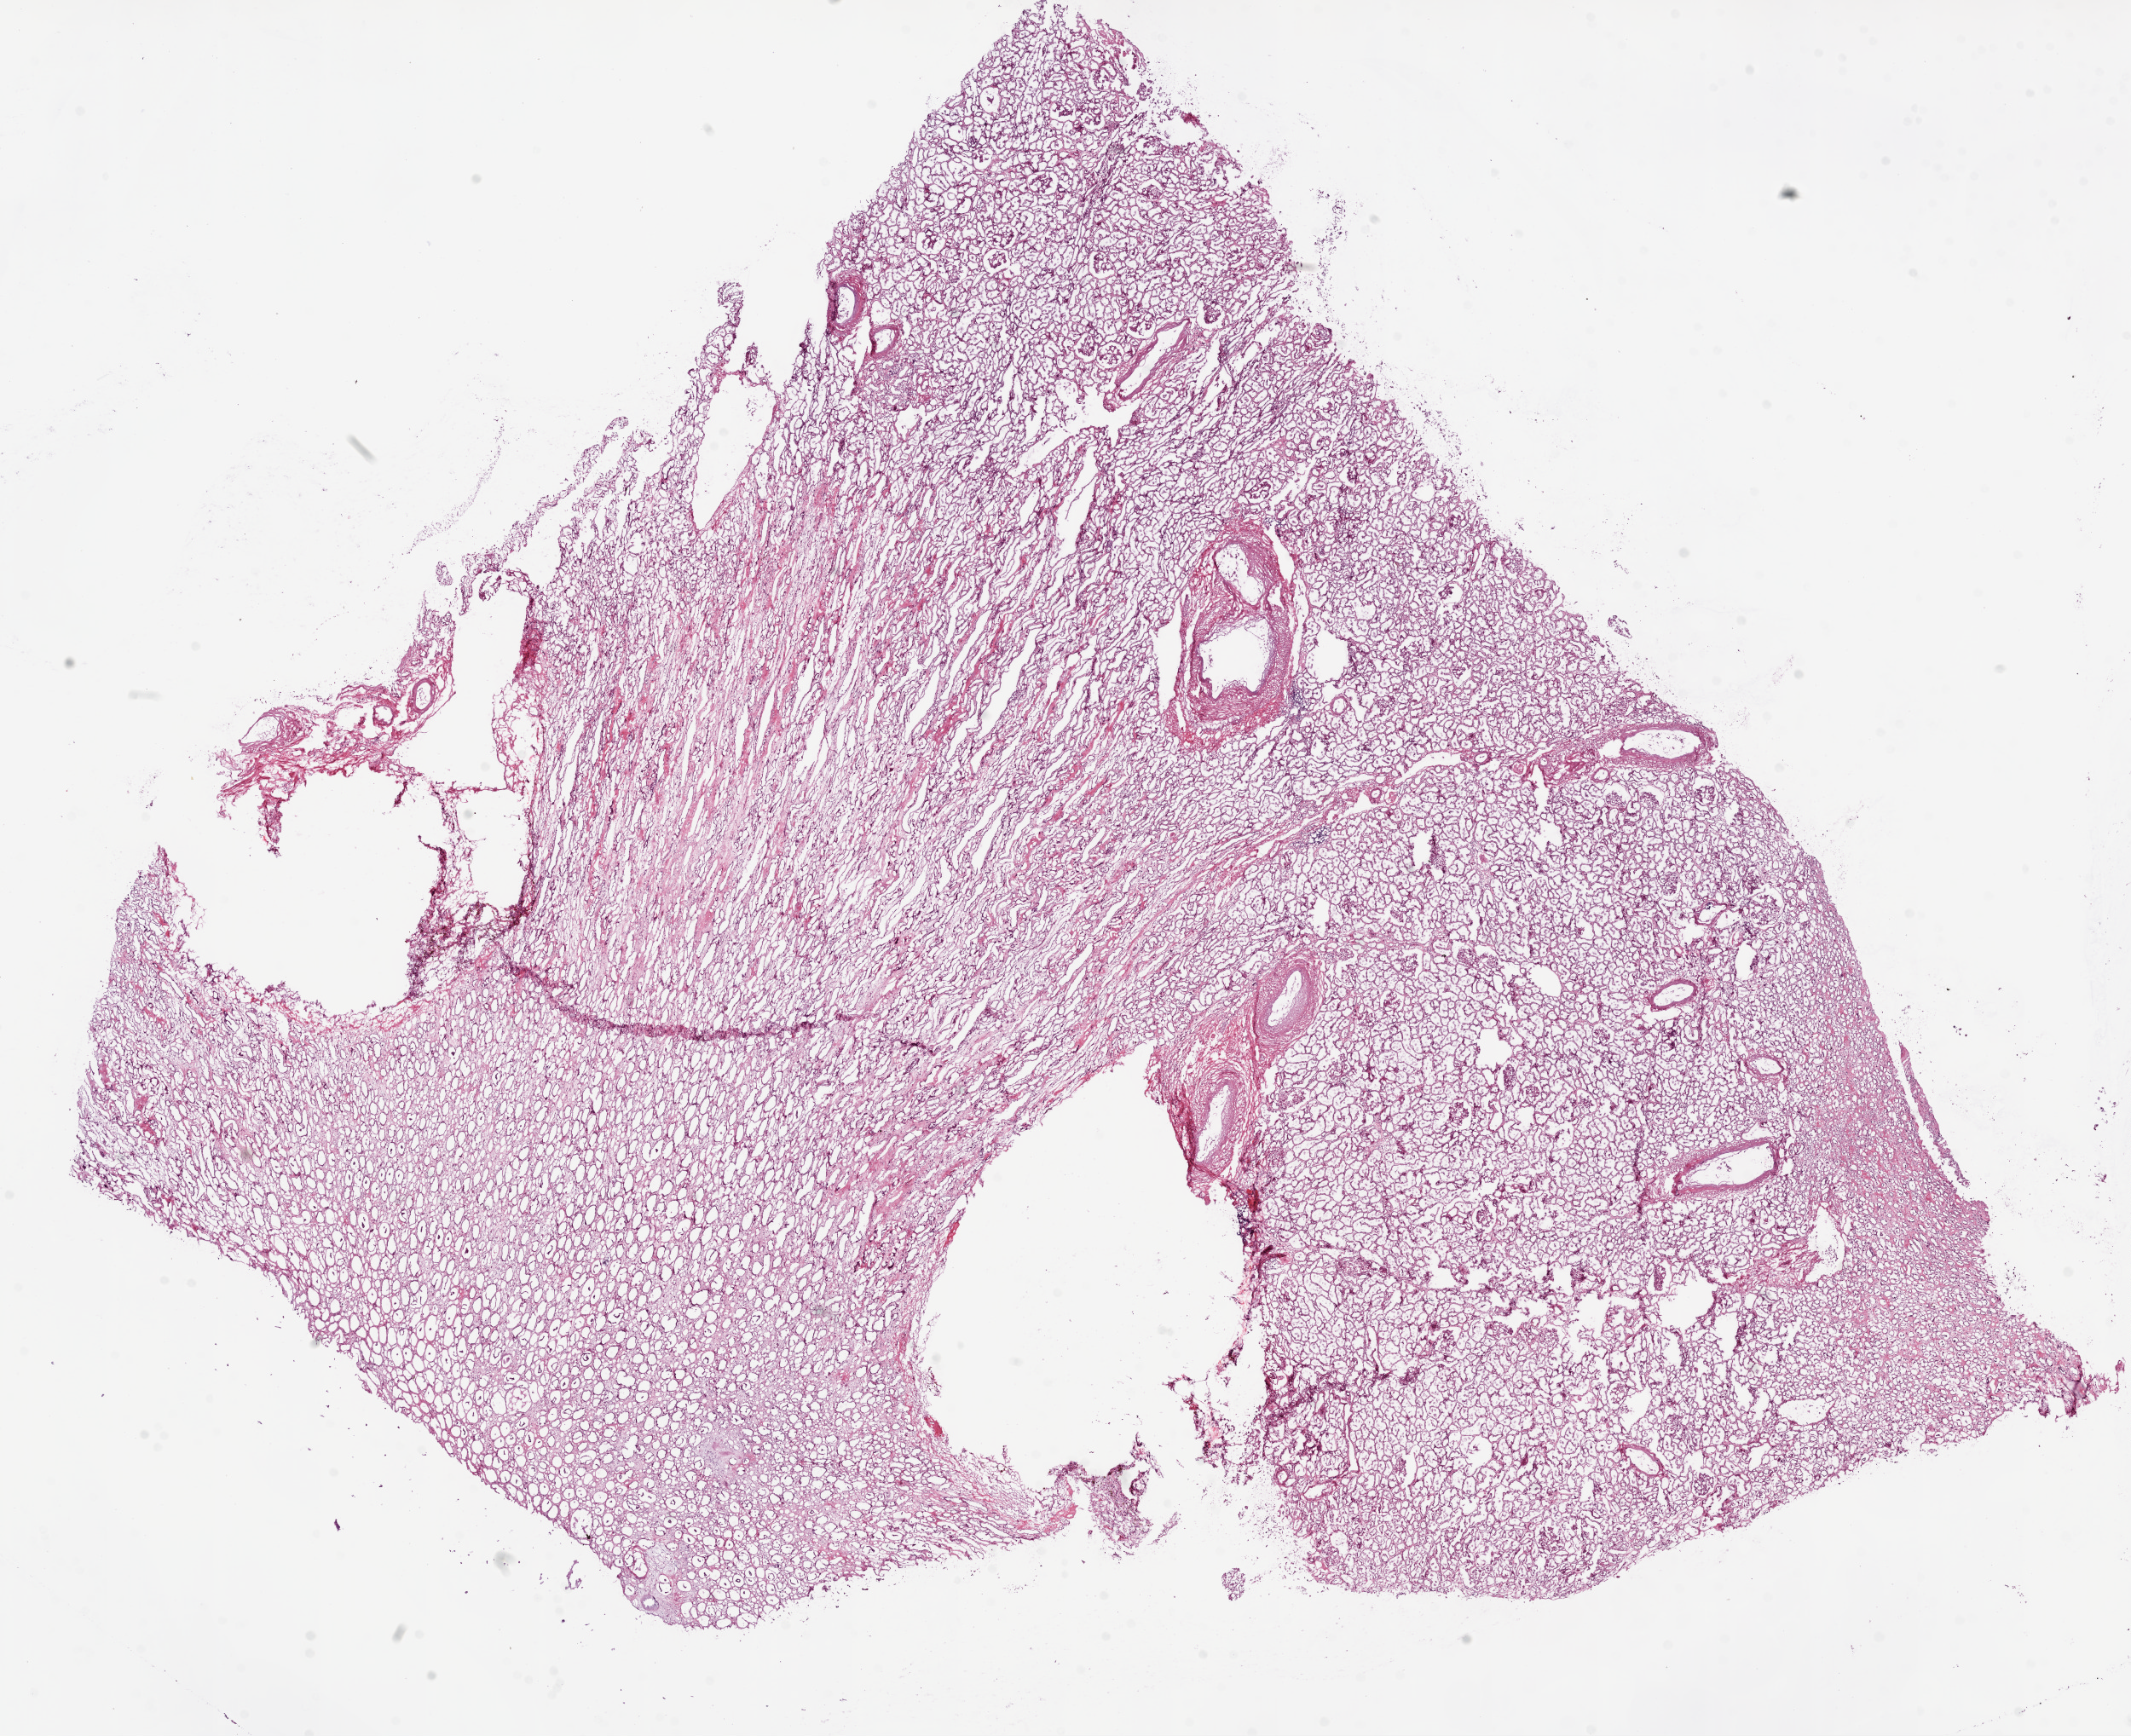
Hematoxylin and eosin (H&E) stained whole-slide image — shown as a low-resolution overview of the whole scanned area (about 20.1 x 16.3 mm, from a 20x scan); frozen section; solid tissue normal (non-tumour tissue) sample from the kidney. Patient: male, age at initial diagnosis 79 years.
This section: solid tissue normal (non-tumour) sample from the same patient. Patient diagnosis: Clear cell adenocarcinoma, NOS.